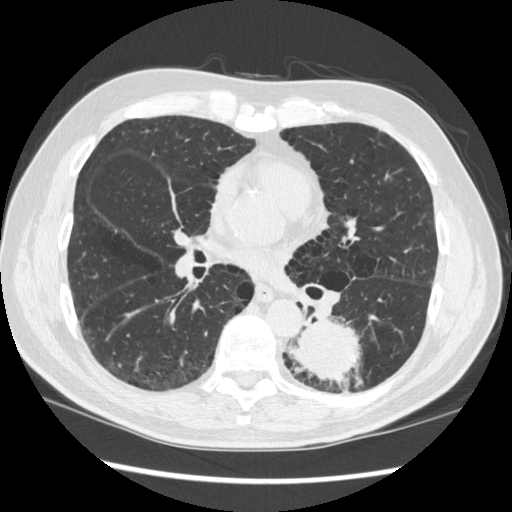
Low-dose screening chest CT, axial slice; baseline annual screen; lung window (W 1500 / L -600 HU); 1.25 mm slice thickness; standard (soft-tissue) reconstruction kernel (STANDARD); slice 160 of 348 in the series. Male, age 72 years at enrolment. Current smoker at enrolment.
Lesion marked by an expert reader, bounding box <265,305,369,397> (left, top, right, bottom; pixels). The screening reader recorded 2 non-calcified nodules or masses ≥4 mm on this exam (left lower lobe, right middle lobe); which of them this box marks is not recorded. Participant outcome: lung cancer diagnosed 37 days after this screen — squamous cell carcinoma, NOS, left lower lobe, stage IIIA (AJCC 6th edition), 60 mm at pathology.